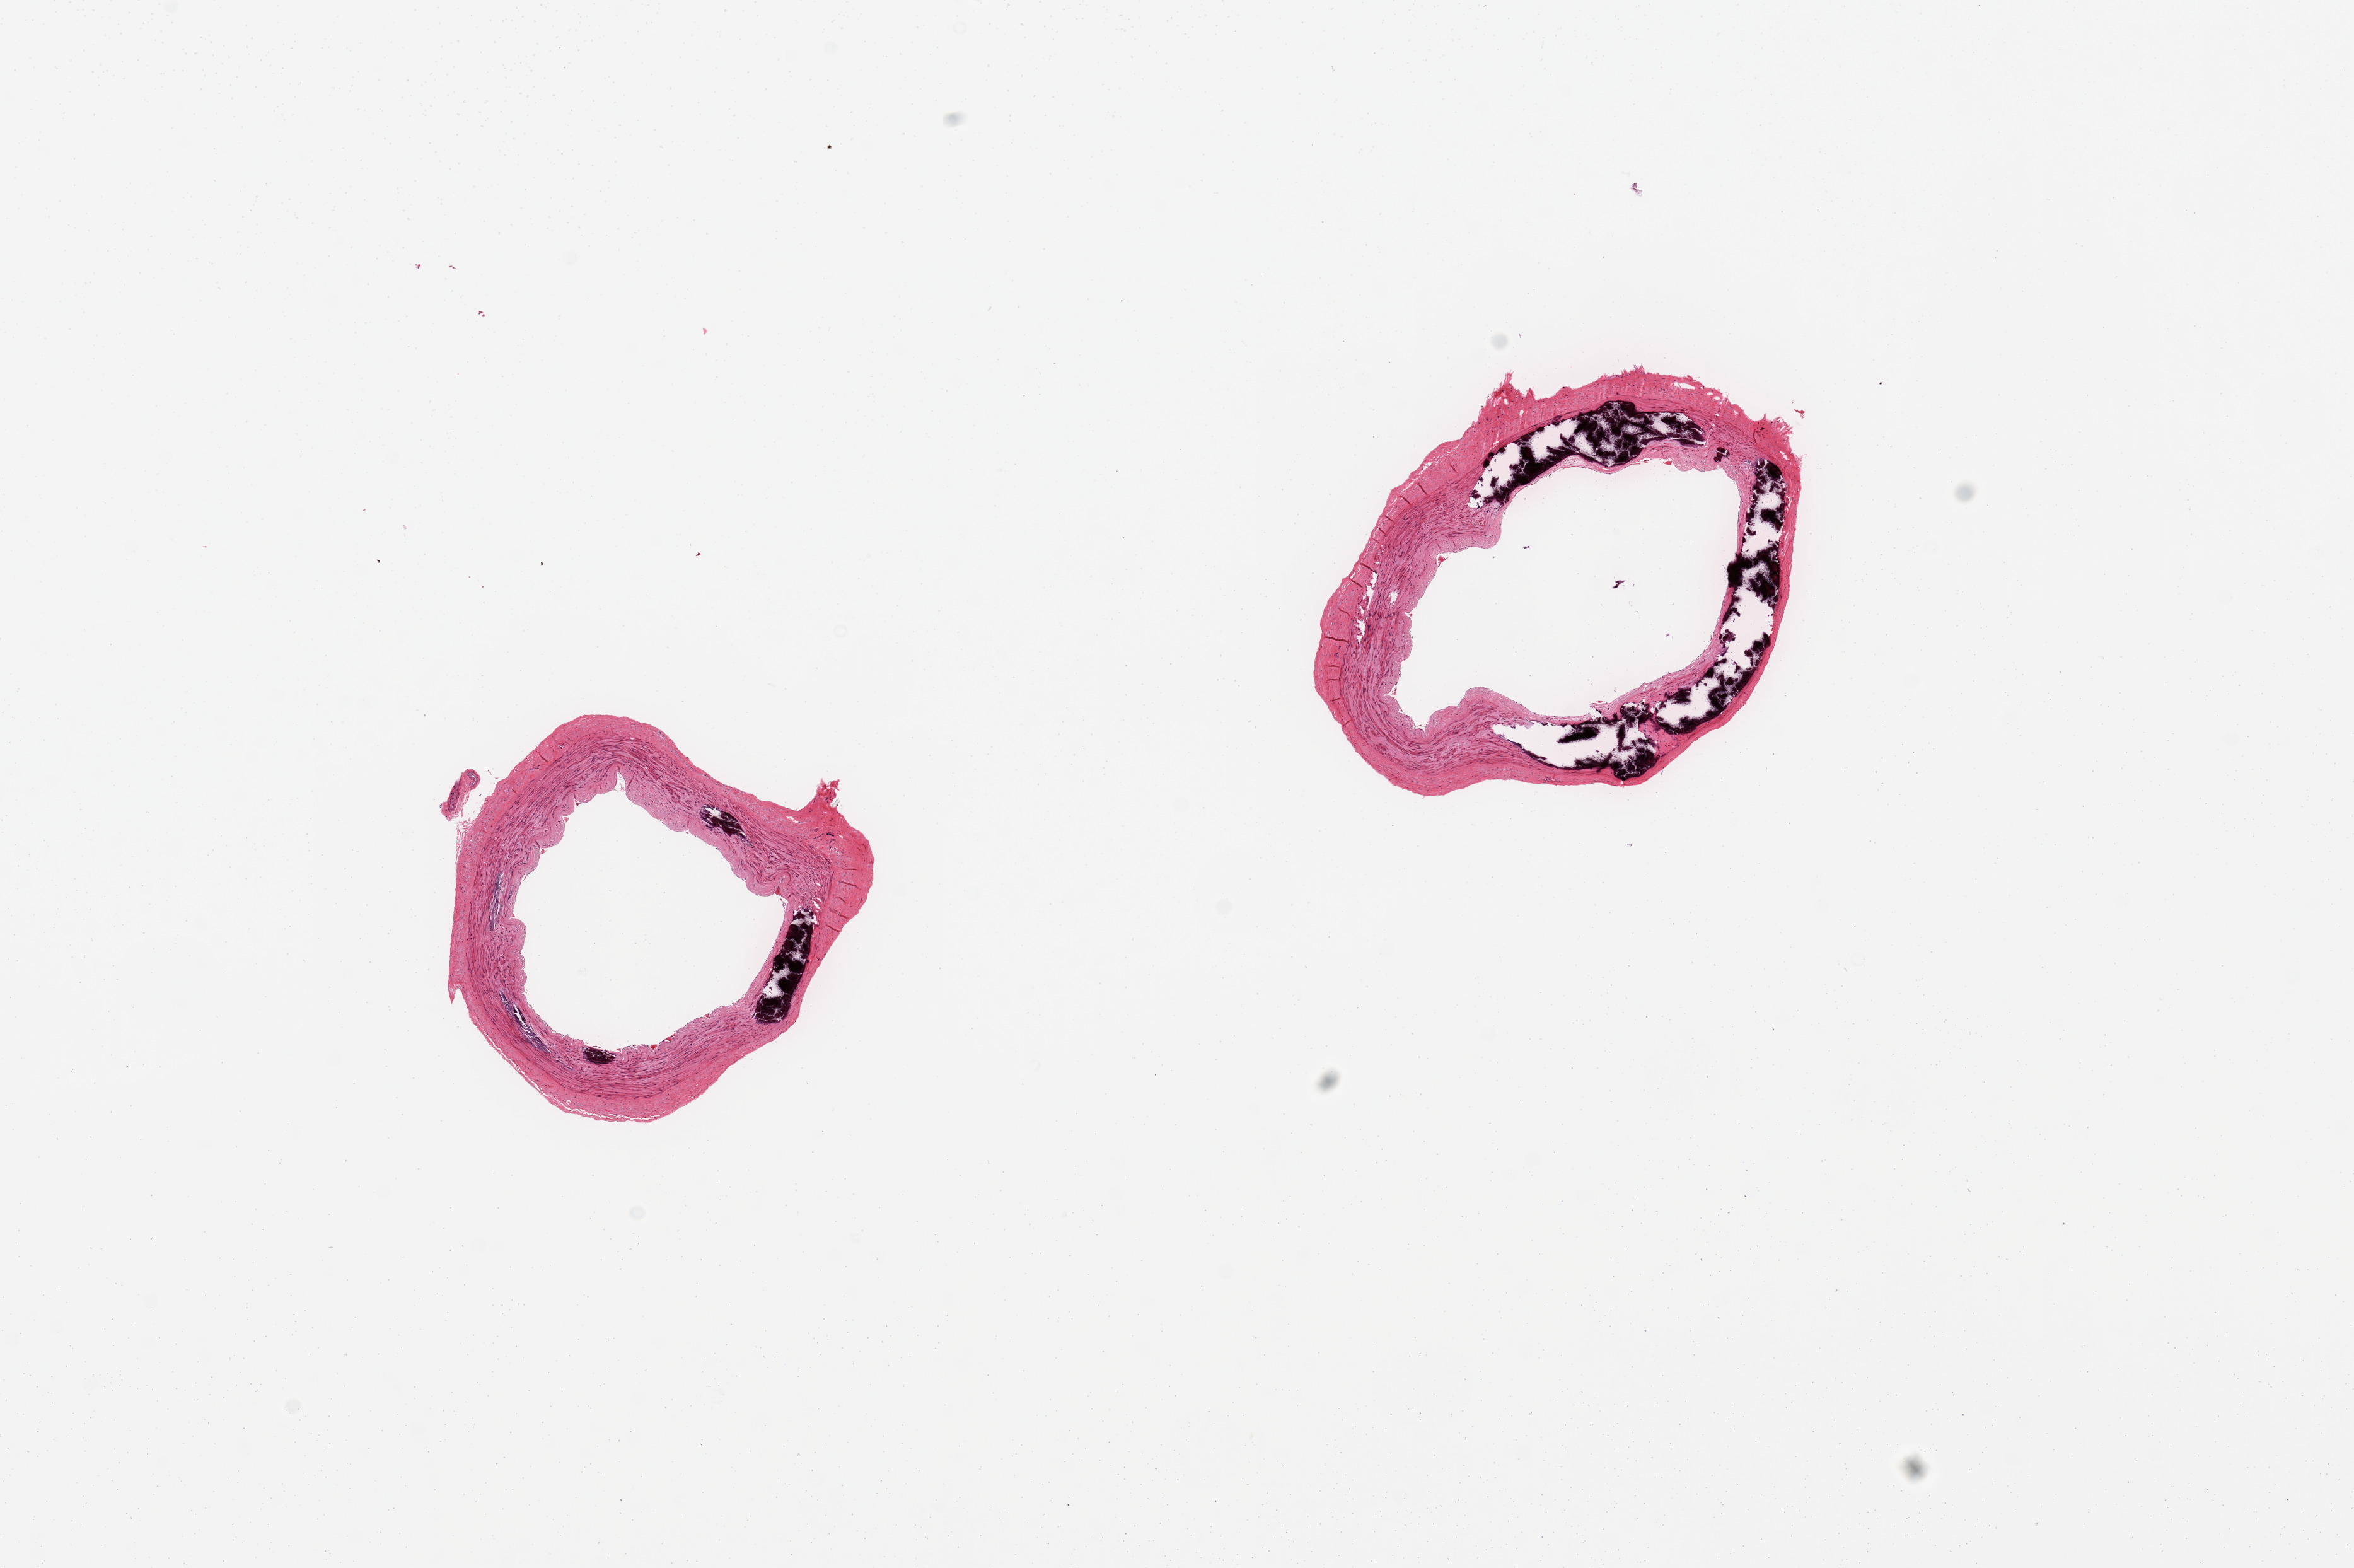
Whole-slide image, haematoxylin and eosin stain — shown as a low-resolution overview of the whole scanned area (about 14.8 x 9.8 mm, from a 20x scan). PAXgene-fixed, paraffin-embedded tissue. Target tissue: tibial artery. Donor tissue sample.
Review note (as recorded): 2 pieces, prominent Monkeberg medial sclerosis; non adherent fat or significant atherosis.